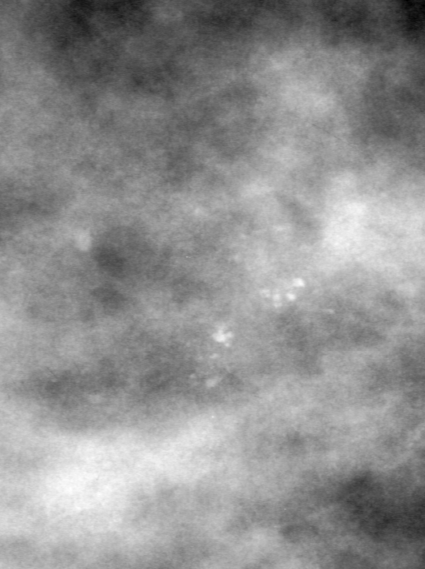
Cropped region of a digitized screen-film mammogram centred on a radiologist-marked abnormality, left breast, CC view.
Marked abnormality: calcifications, morphology pleomorphic, distribution clustered; BI-RADS assessment category 4; pathology result (as recorded, not read from the image): malignant.